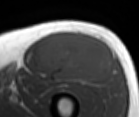
MRI of an extremity soft-tissue mass, one axial slice. MR volume resampled by the dataset authors to the PET/CT grid (not the native acquisition matrix). 3.27 mm slice thickness. 139 × 117 image matrix. Male patient. From the clinical record (not read from this slice): histological type: extraskeletal osteosarcoma; grade: high; site of the primary tumour: thigh.
Outlined on this slice (expert contour drawn on MRI and transferred to this co-registered scan by the dataset authors):
- gross tumour volume (mass): box from (x=38, y=32) to (x=114, y=83) px